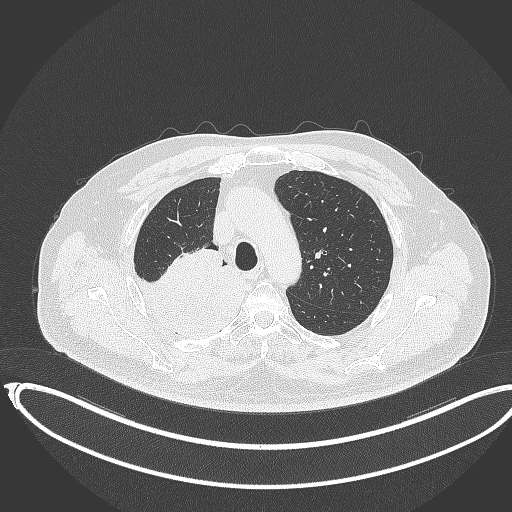
Chest CT, one axial slice; position 271 of 403 along the scan axis; 120 kVp; lung window (W 1500 / L -600 HU); 512 × 512 image matrix. Patient: male, 68 years. From the clinical record (not read from this slice): clinical TNM (as recorded): T2a N0 M0.
Structures marked on this image (rectangle marked by the reading radiologist):
- lung tumour (recorded histology: adenocarcinoma): bounding box (x1, y1, x2, y2) in pixels: (131, 249, 246, 342)